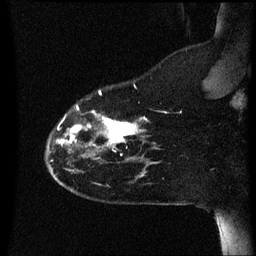
Breast MRI (dynamic contrast-enhanced), one sagittal slice. Slice 12 of 60 in the series (ordered by position). Dynamic contrast-enhanced series, image 2 of 3 at this slice position (ordered by acquisition). 1.5 T. TE 4.2 ms, TR 8.4 ms. 2.2 mm slice thickness. 256 × 256 image matrix, field of view 200 × 200 mm. Patient: female, 35 years. From the clinical record (not read from this slice): setting: breast cancer imaged before/during neoadjuvant chemotherapy; receptor status: HER2-positive.
Outlined on this slice (semi-automatic segmentation, software-assisted and operator-edited):
- analysis volume of interest (the breast-tissue region the enhancement analysis was run in; not a lesion): bounding box <47,82,162,173> (left, top, right, bottom; pixels)
- tumour enhancement mask (voxels above the 70 % enhancement threshold inside the analysis volume of interest): <57,90,149,151>